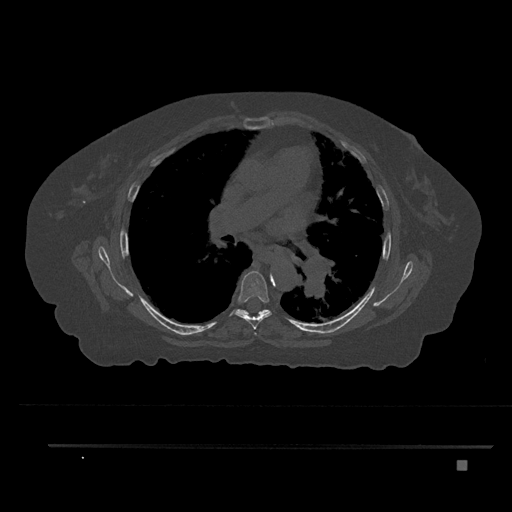
CT including the spine, one axial slice; slice 520 of 797 in the series (ordered by position); reconstruction kernel Br40s/3; bone window (W 1800 / L 400 HU); 0.5 mm slice thickness; 512 × 512 image matrix, field of view 437 × 437 mm. Patient: female, 76 years. Case-level facts recorded for this patient, not image findings: primary cancer: lung; vertebrae with lytic lesions (as recorded): T11, L3.
Annotated regions visible in this slice (semi-automatic segmentation, software-assisted and operator-edited):
- T5 vertebra: bounding box <254,332,257,335> (left, top, right, bottom; pixels)
- T6 vertebra: <235,271,272,329>
- T7 vertebra: <237,309,269,317>